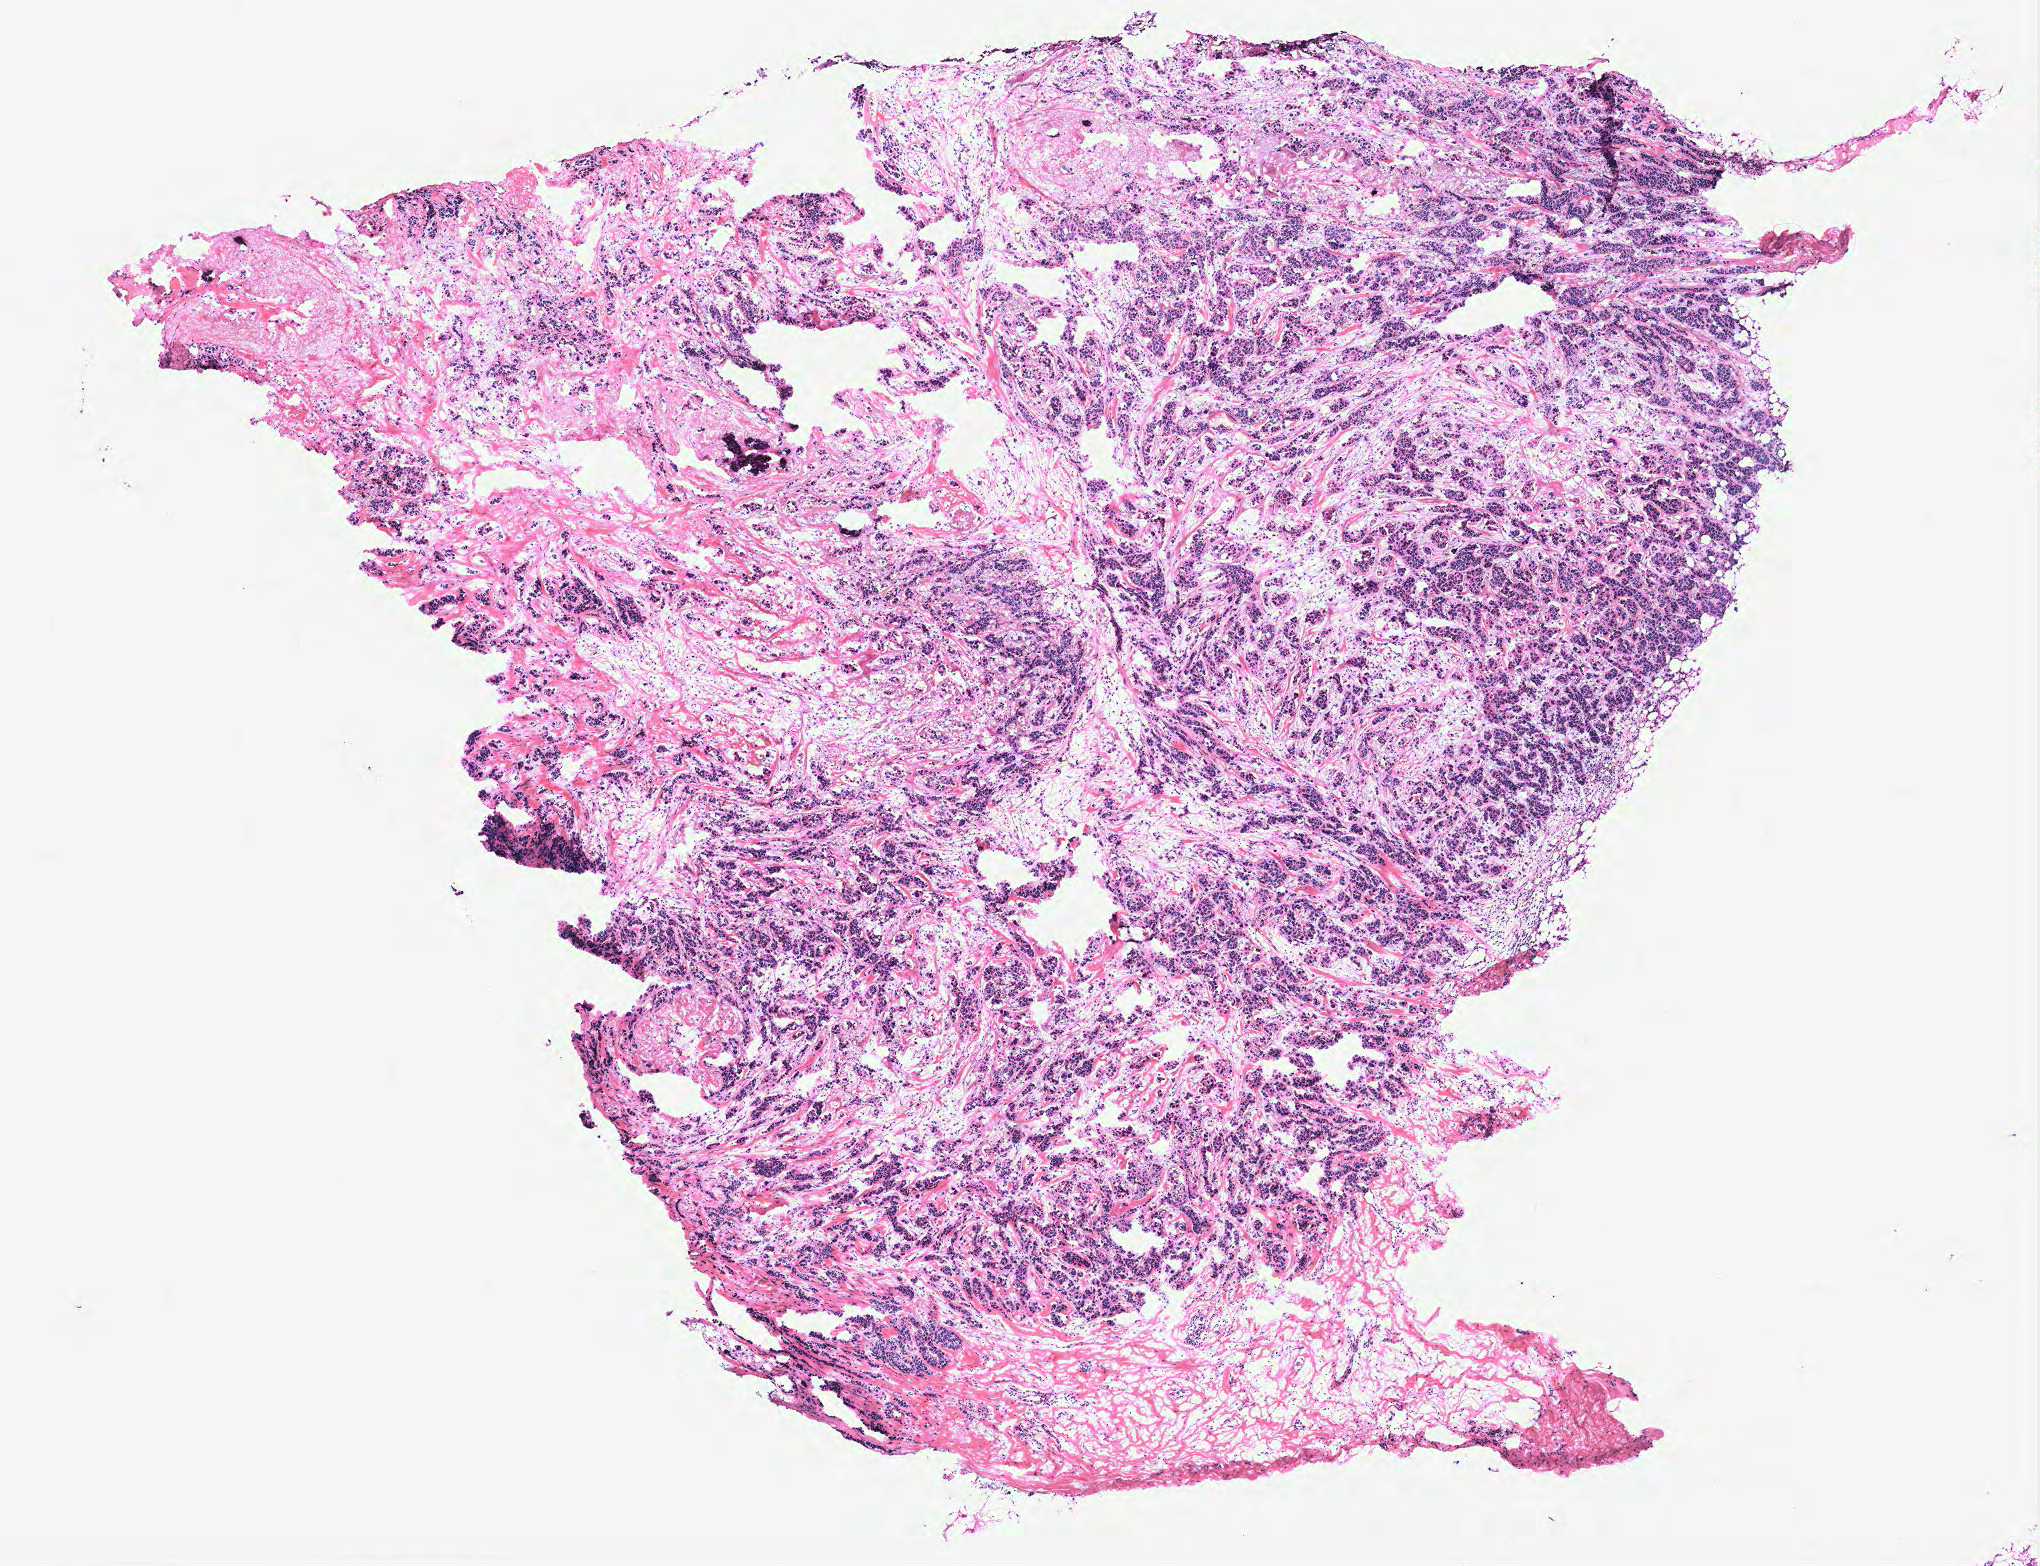
Digitized Hematoxylin and eosin (H&E) stained tissue section (whole slide) — a low-resolution overview of the entire scanned area, about 8.2 x 6.3 mm (from a 40x scan), breast, tissue type not recorded.
Patient diagnosis (cohort enrolment): breast cancer (breast).